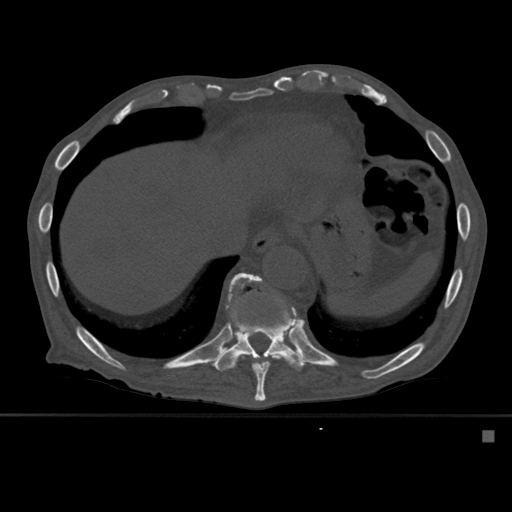
CT including the spine, one axial slice. Bone window (W 1800 / L 400 HU). 1.5 mm slice thickness. 512 × 512 image matrix, field of view 373 × 373 mm. Male patient, age 78 years. Case-level facts recorded for this patient, not image findings: primary cancer: prostate.
Annotated regions visible in this slice (semi-automatically segmented with operator editing):
- T10 vertebra: bounding box <226,273,299,401> (left, top, right, bottom; pixels)
- T11 vertebra: <213,274,309,371>